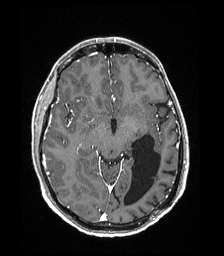
Brain MRI from a brain-tumour surgery series, one axial slice; slice 104 of 192 in the series (ordered by position); T1-weighted post-contrast; 1 mm slice thickness; 224 × 256 image matrix. From the clinical record (not read from this slice): histopathology: Low grade glioma; IDH mutation: no.
Annotated regions visible in this slice (outlined manually by an expert reader):
- previous resection cavity: box from (x=124, y=134) to (x=161, y=206) px